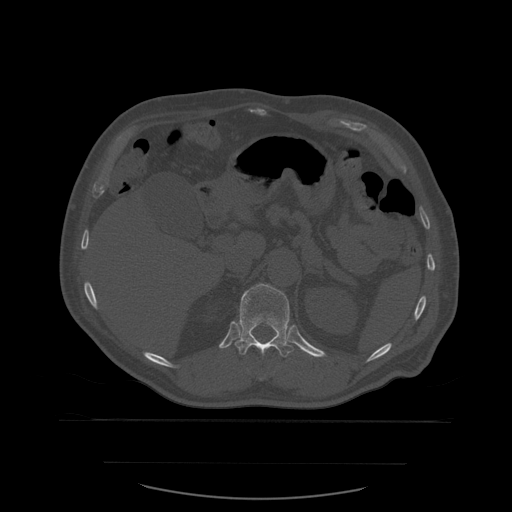
CT including the spine, one axial slice. Position 274 of 590 along the scan axis. Bone window (W 1800 / L 400 HU). 1.25 mm slice thickness. 512 × 512 image matrix. Patient age 71 years. From the clinical record (not read from this slice): primary cancer: lung.
Structures marked on this image (semi-automatically segmented with operator editing):
- T11 vertebra: box from (x=260, y=378) to (x=263, y=381) px
- T12 vertebra: (x=235, y=284)–(x=294, y=358)